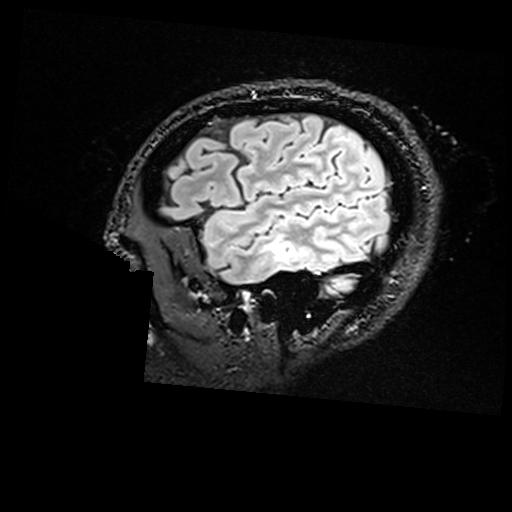
Brain MRI from a brain-tumour surgery series, one sagittal slice; T2 FLAIR; 1 mm slice thickness; 512 × 512 image matrix, field of view 250 × 250 mm. Case-level facts recorded for this patient, not image findings: histopathology: Non-tumor destructive chronic inflammatory lesion with abnormal vasculature; tumour location: Right Inferior Temporal.
Structures marked on this image (manually delineated by an expert):
- residual tumour: bounding box <280,241,296,259> (left, top, right, bottom; pixels)